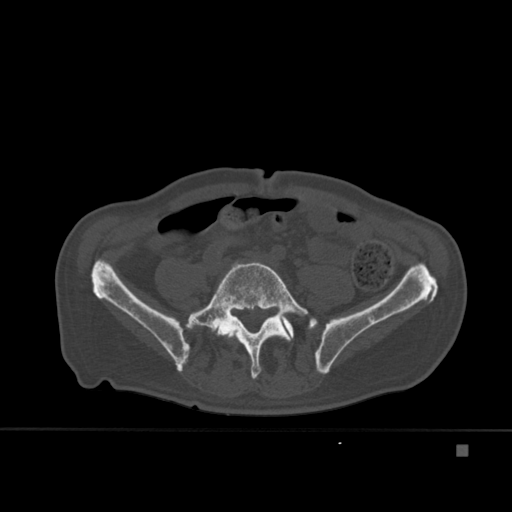
CT including the spine, one axial slice; slice 104 of 451 in the series (ordered by position); bone window (W 1800 / L 400 HU); 512 × 512 image matrix, field of view 378 × 378 mm. Male patient, age 75 years. From the clinical record (not read from this slice): primary cancer: prostate.
Outlined on this slice (semi-automatically segmented with operator editing):
- L4 vertebra: box from (x=227, y=334) to (x=231, y=338) px
- L5 vertebra: (x=186, y=262)–(x=308, y=379)
- T7 vertebra: (x=211, y=294)–(x=243, y=324)